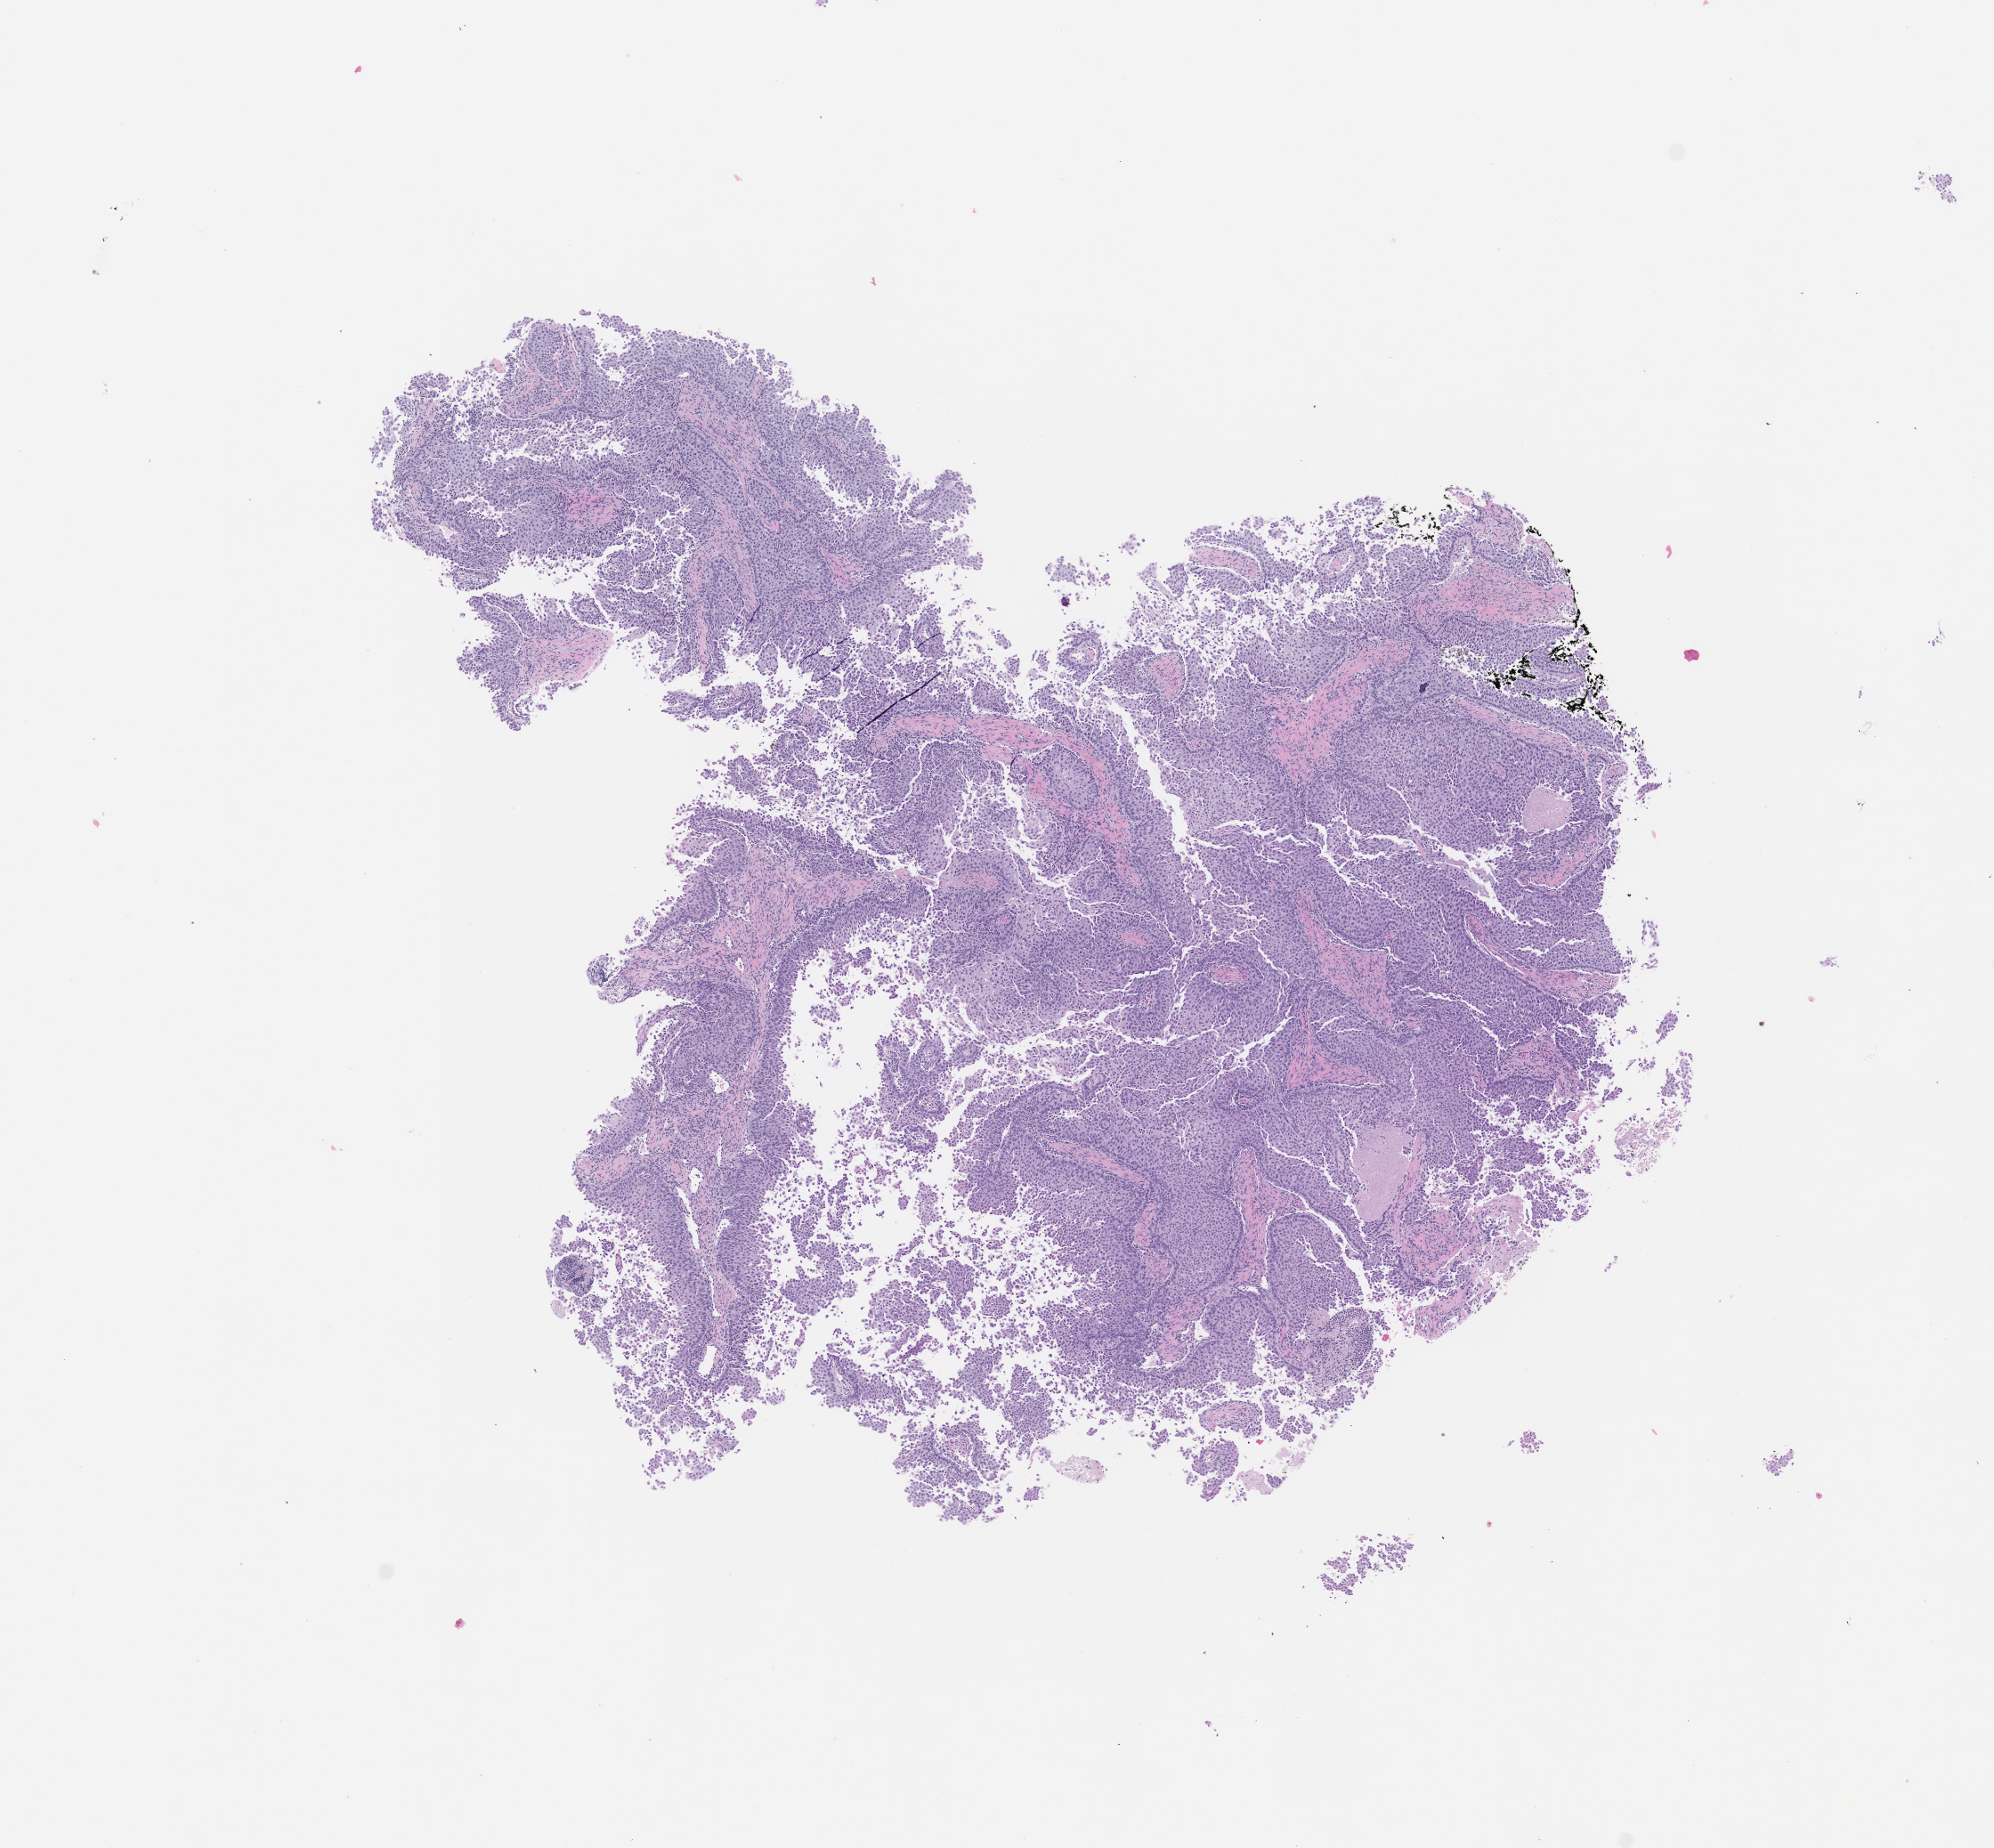
Haematoxylin and eosin whole-slide image of a patient-derived xenograft (PDX) tumor grown in a mouse, passage 3, whole scanned area (about 9.0 x 8.3 mm) shown as a low-resolution overview; formalin-fixed, paraffin-embedded (FFPE) tissue; tumor site category: bladder.
Originating patient diagnosis: Urothelial Carcinoma.